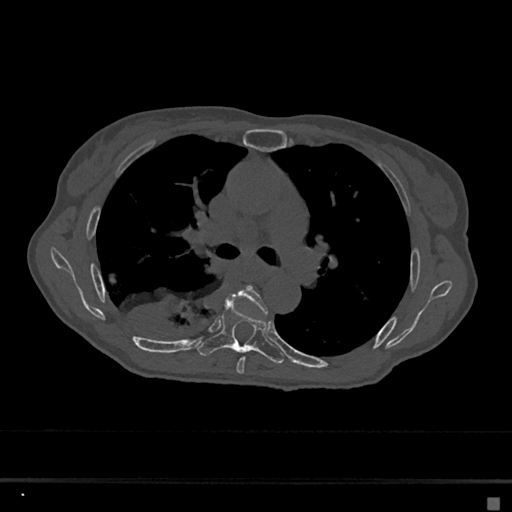
CT including the spine, one axial slice. Slice 433 of 797 in the series (ordered by position). Reconstruction kernel Br40s/3. 120 kVp. Bone window (W 1800 / L 400 HU). 0.5 mm slice thickness. 512 × 512 image matrix. Patient: female, 68 years. From the clinical record (not read from this slice): primary cancer: renal.
Structures marked on this image (semi-automatic segmentation, software-assisted and operator-edited):
- T5 vertebra: box from (x=228, y=285) to (x=268, y=375) px
- T6 vertebra: (x=197, y=299)–(x=284, y=364)